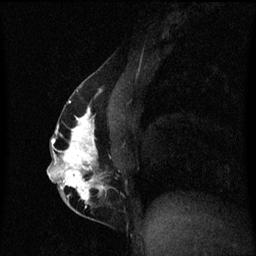
Breast MRI (dynamic contrast-enhanced), one sagittal slice. Position 29 of 60 along the scan axis. Dynamic contrast-enhanced series, image 2 of 3 at this slice position (ordered by acquisition). 1.5 T. TE 4.2 ms, TR 8.4 ms. 2 mm slice thickness. 256 × 256 image matrix. Patient: female, 40 years.
Annotated regions visible in this slice (semi-automatic segmentation, software-assisted and operator-edited):
- analysis volume of interest (the breast-tissue region the enhancement analysis was run in; not a lesion): bounding box (x1, y1, x2, y2) in pixels: (48, 84, 122, 211)
- tumour enhancement mask (voxels above the 70 % enhancement threshold inside the analysis volume of interest): (48, 90, 107, 209)